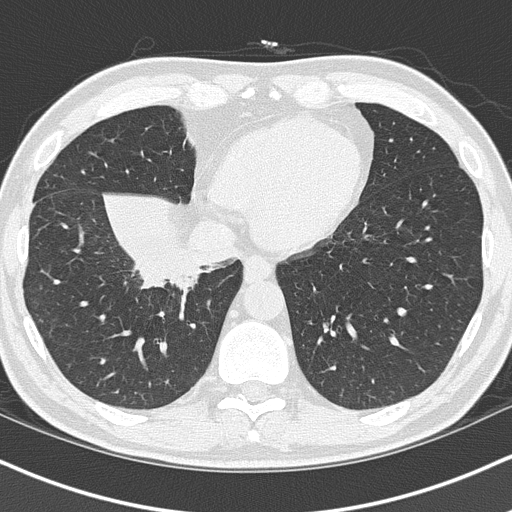
Low-dose screening chest CT, axial slice; first (baseline) screen; lung window (W 1500 / L -600 HU); slice 35 of 151 in the series; 512 × 512 image matrix. Male, age 55 years at enrolment. Current smoker at enrolment.
Expert reader's lesion annotation, bounding box (x1, y1, x2, y2) in pixels: (116, 221, 246, 320). Screening reader's record for this exam (one nodule recorded; not confirmed to be the boxed lesion): non-calcified nodule or mass ≥4 mm, right lower lobe, 6 × 5 mm, spiculated (stellate) margins, soft tissue attenuation. Official screen result: positive, change unspecified: nodule(s) >= 4 mm or enlarging nodule(s), mass(es), or other non-specific abnormalities suspicious for lung cancer.